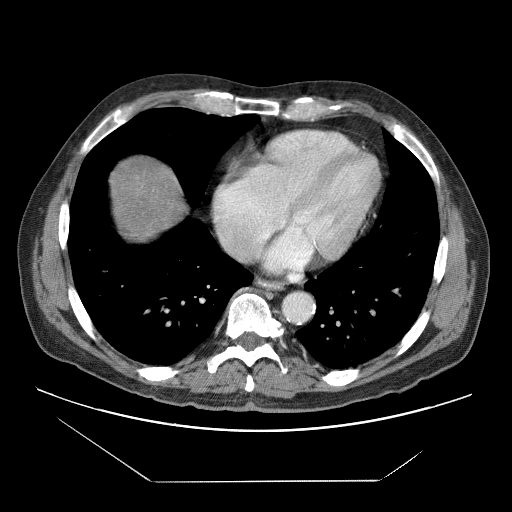
Contrast-enhanced abdominal CT (liver protocol), one axial slice; slice 74 of 83 in the series (ordered by position); 120 kVp; soft-tissue window (W 400 / L 40 HU); 512 × 512 image matrix, field of view 420 × 420 mm. Case-level facts recorded for this patient, not image findings: diagnosis: hepatocellular carcinoma (patient treated with transarterial chemoembolisation; whether this scan precedes or follows treatment is not stated here); TNM stage (as recorded): Stage-IVB; Child-Pugh class: B.
Annotated regions visible in this slice (semi-automatic segmentation, software-assisted and operator-edited):
- abdominal aorta: bounding box (x1, y1, x2, y2) in pixels: (284, 293, 313, 321)
- liver parenchyma outside the tumour (the mass and vessels are separate outlines, so this box may not span the whole liver): (112, 156, 186, 240)